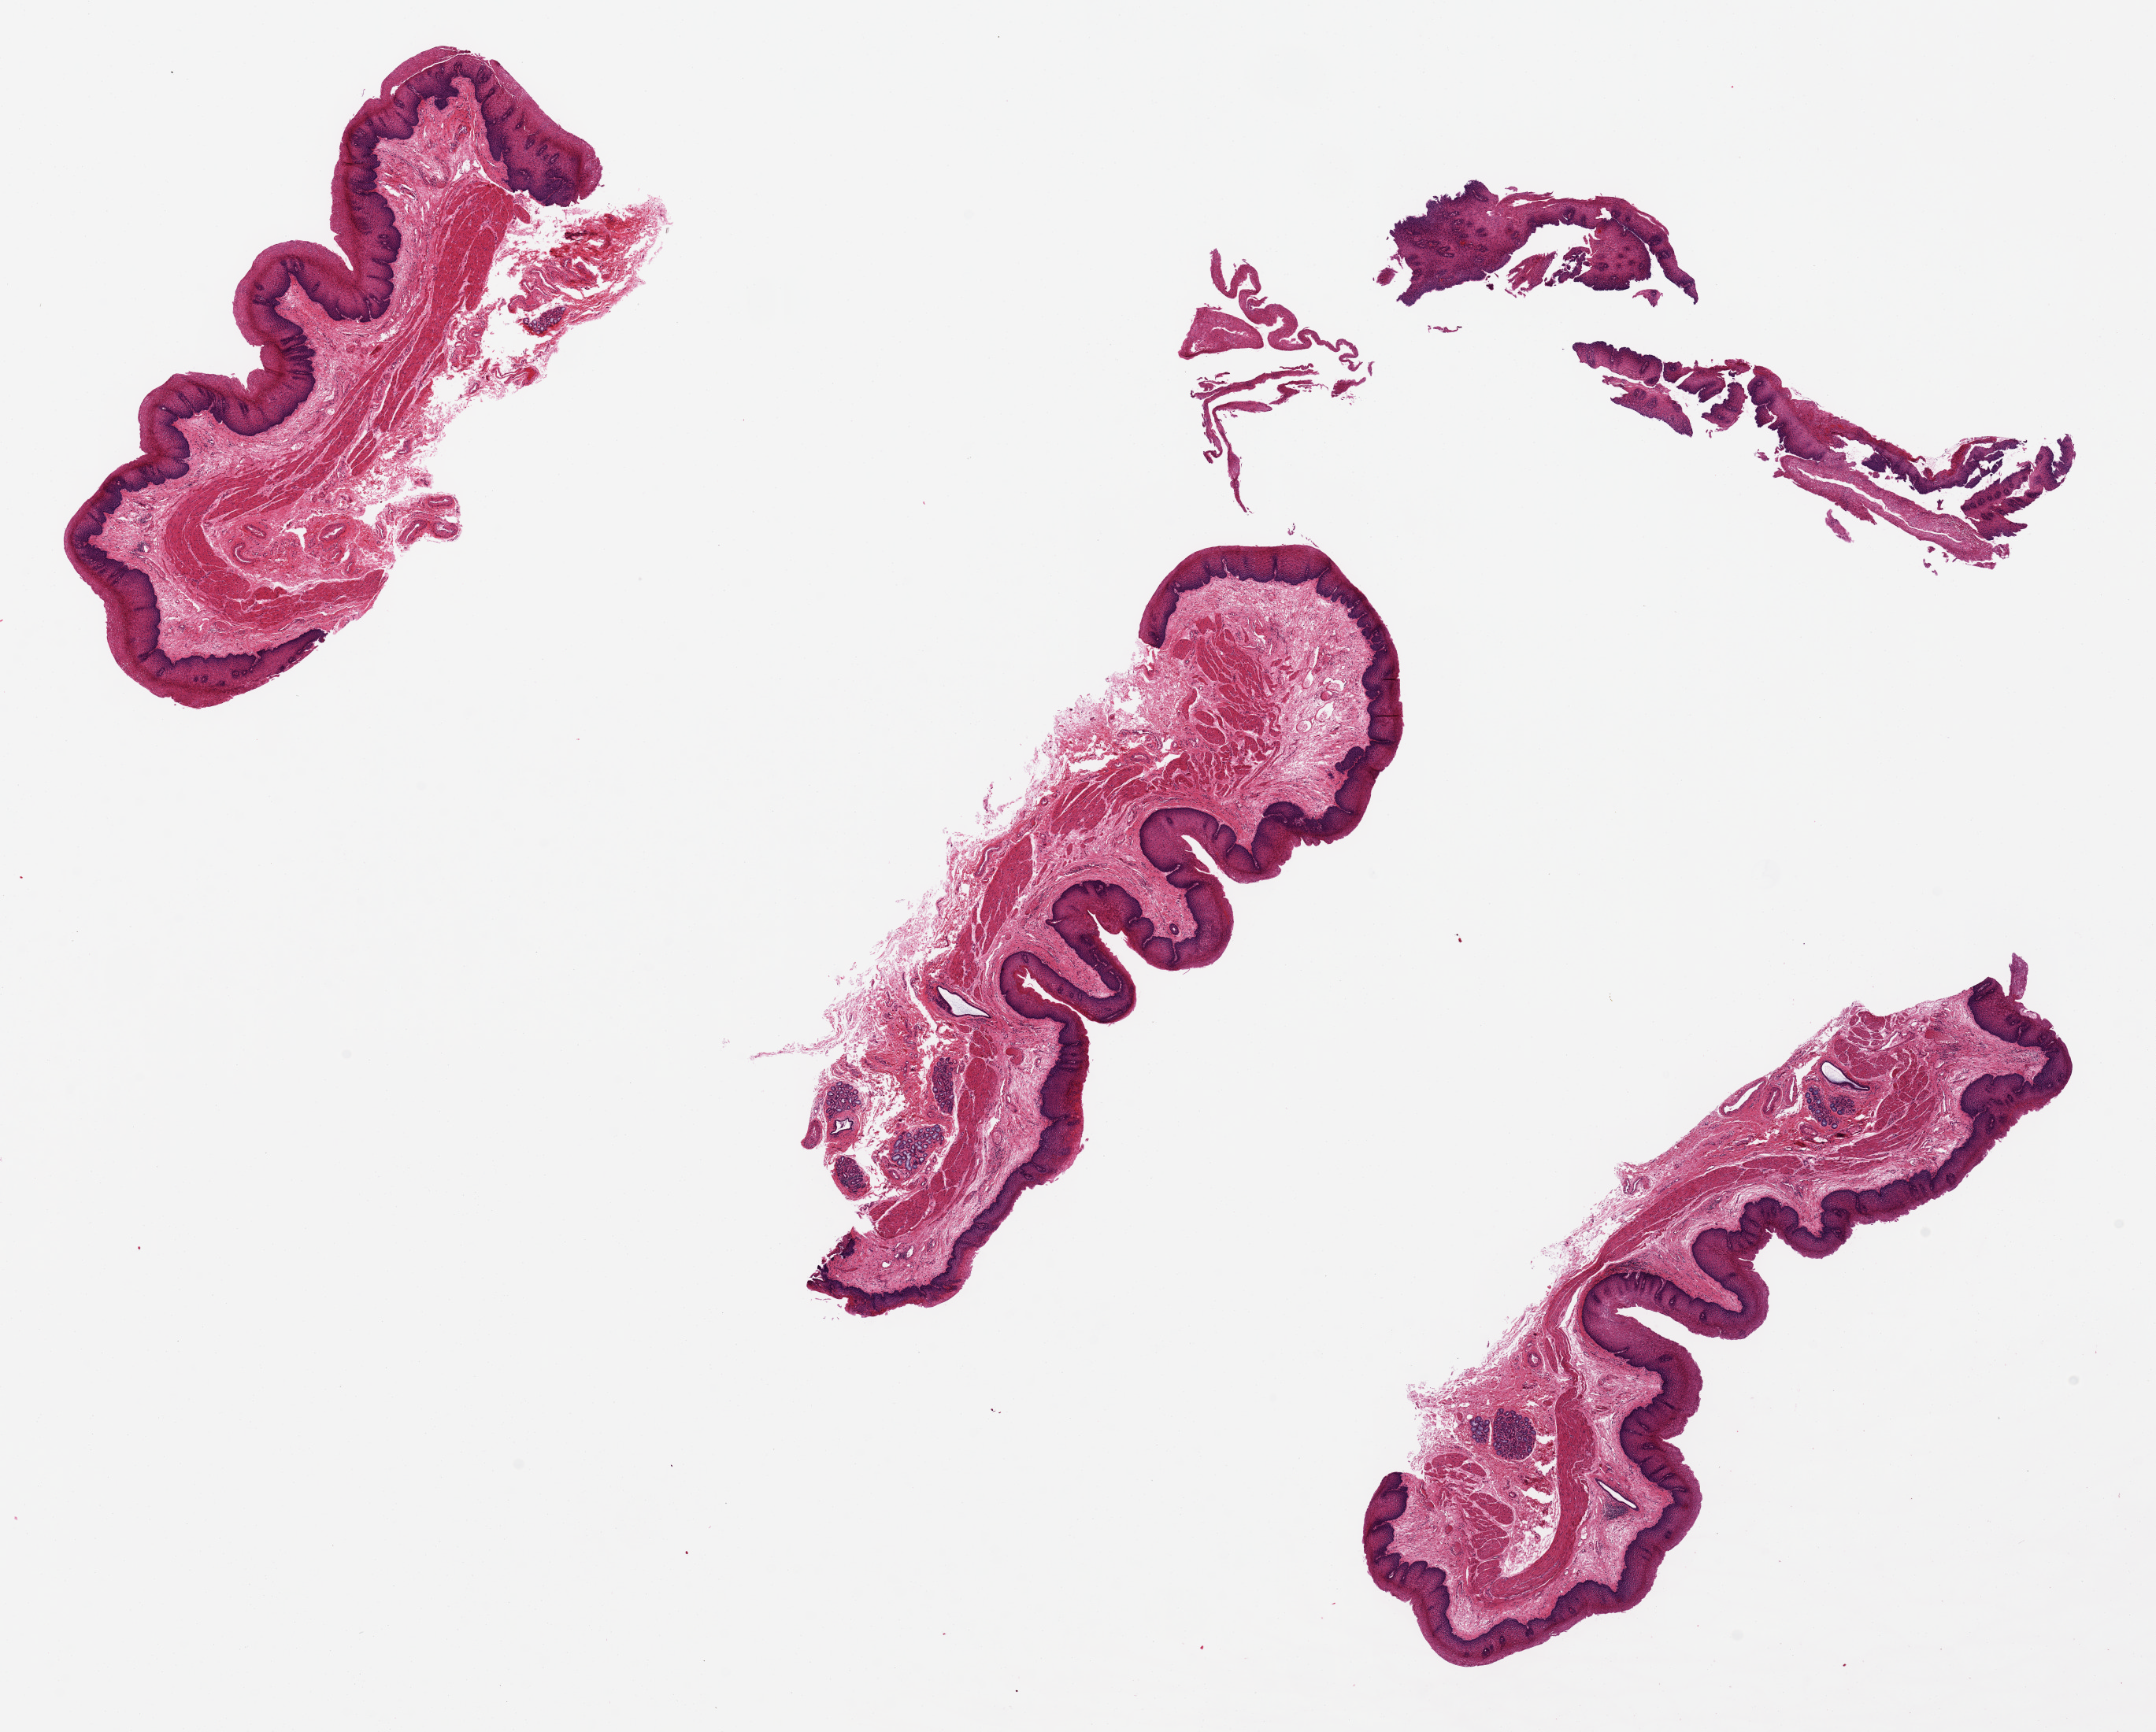
H&E whole-slide image — a low-resolution overview of the entire scanned area, about 21.7 x 17.4 mm; PAXgene-fixed, paraffin-embedded tissue; section of esophageal mucous membrane (target tissue); donor tissue sample. Donor sex: male.
Pathologist's review note for this sample: Epithelial thickness 400-500 microns, 20-30% of section thickness. Focal soft tissue areas appear underfixed.